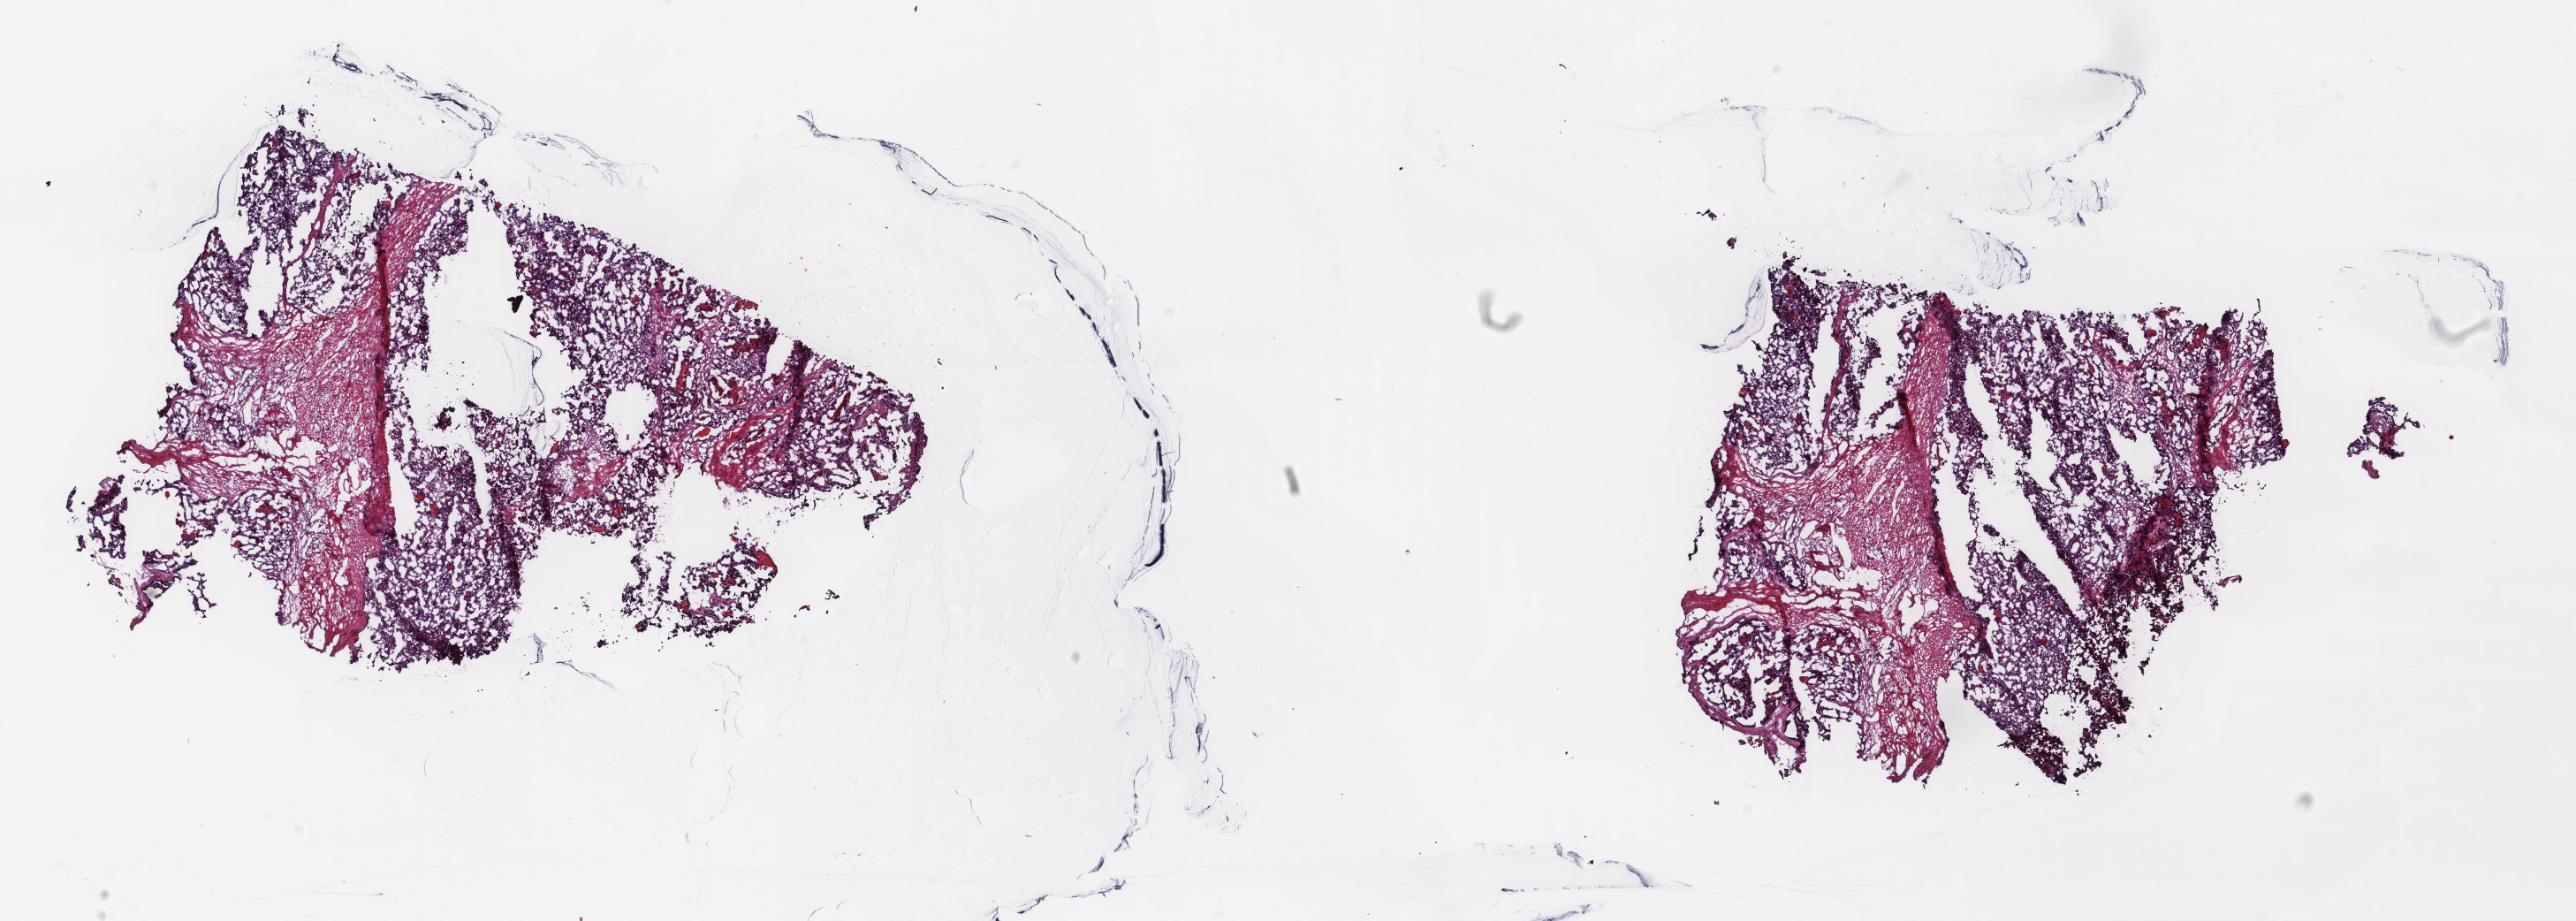
Digitized H&E tissue section (whole slide), low-resolution overview of the scanned area, about 23.1 x 8.3 mm. Frozen section from the top of the tissue portion. Sample: primary tumour, rectum. Patient: female, age at initial diagnosis 77 years. Pathologist review of this section (percent, as recorded): tumour cells 100%, tumour nuclei 80%, normal cells 0%, stromal cells 0%, necrosis 0%. Inflammatory infiltration, as recorded: lymphocyte infiltration 0%, monocyte infiltration 0%, neutrophil infiltration 0%.
- AJCC pathologic stage: IIIB
- pathologic diagnosis: Adenocarcinoma, NOS (rectosigmoid junction)